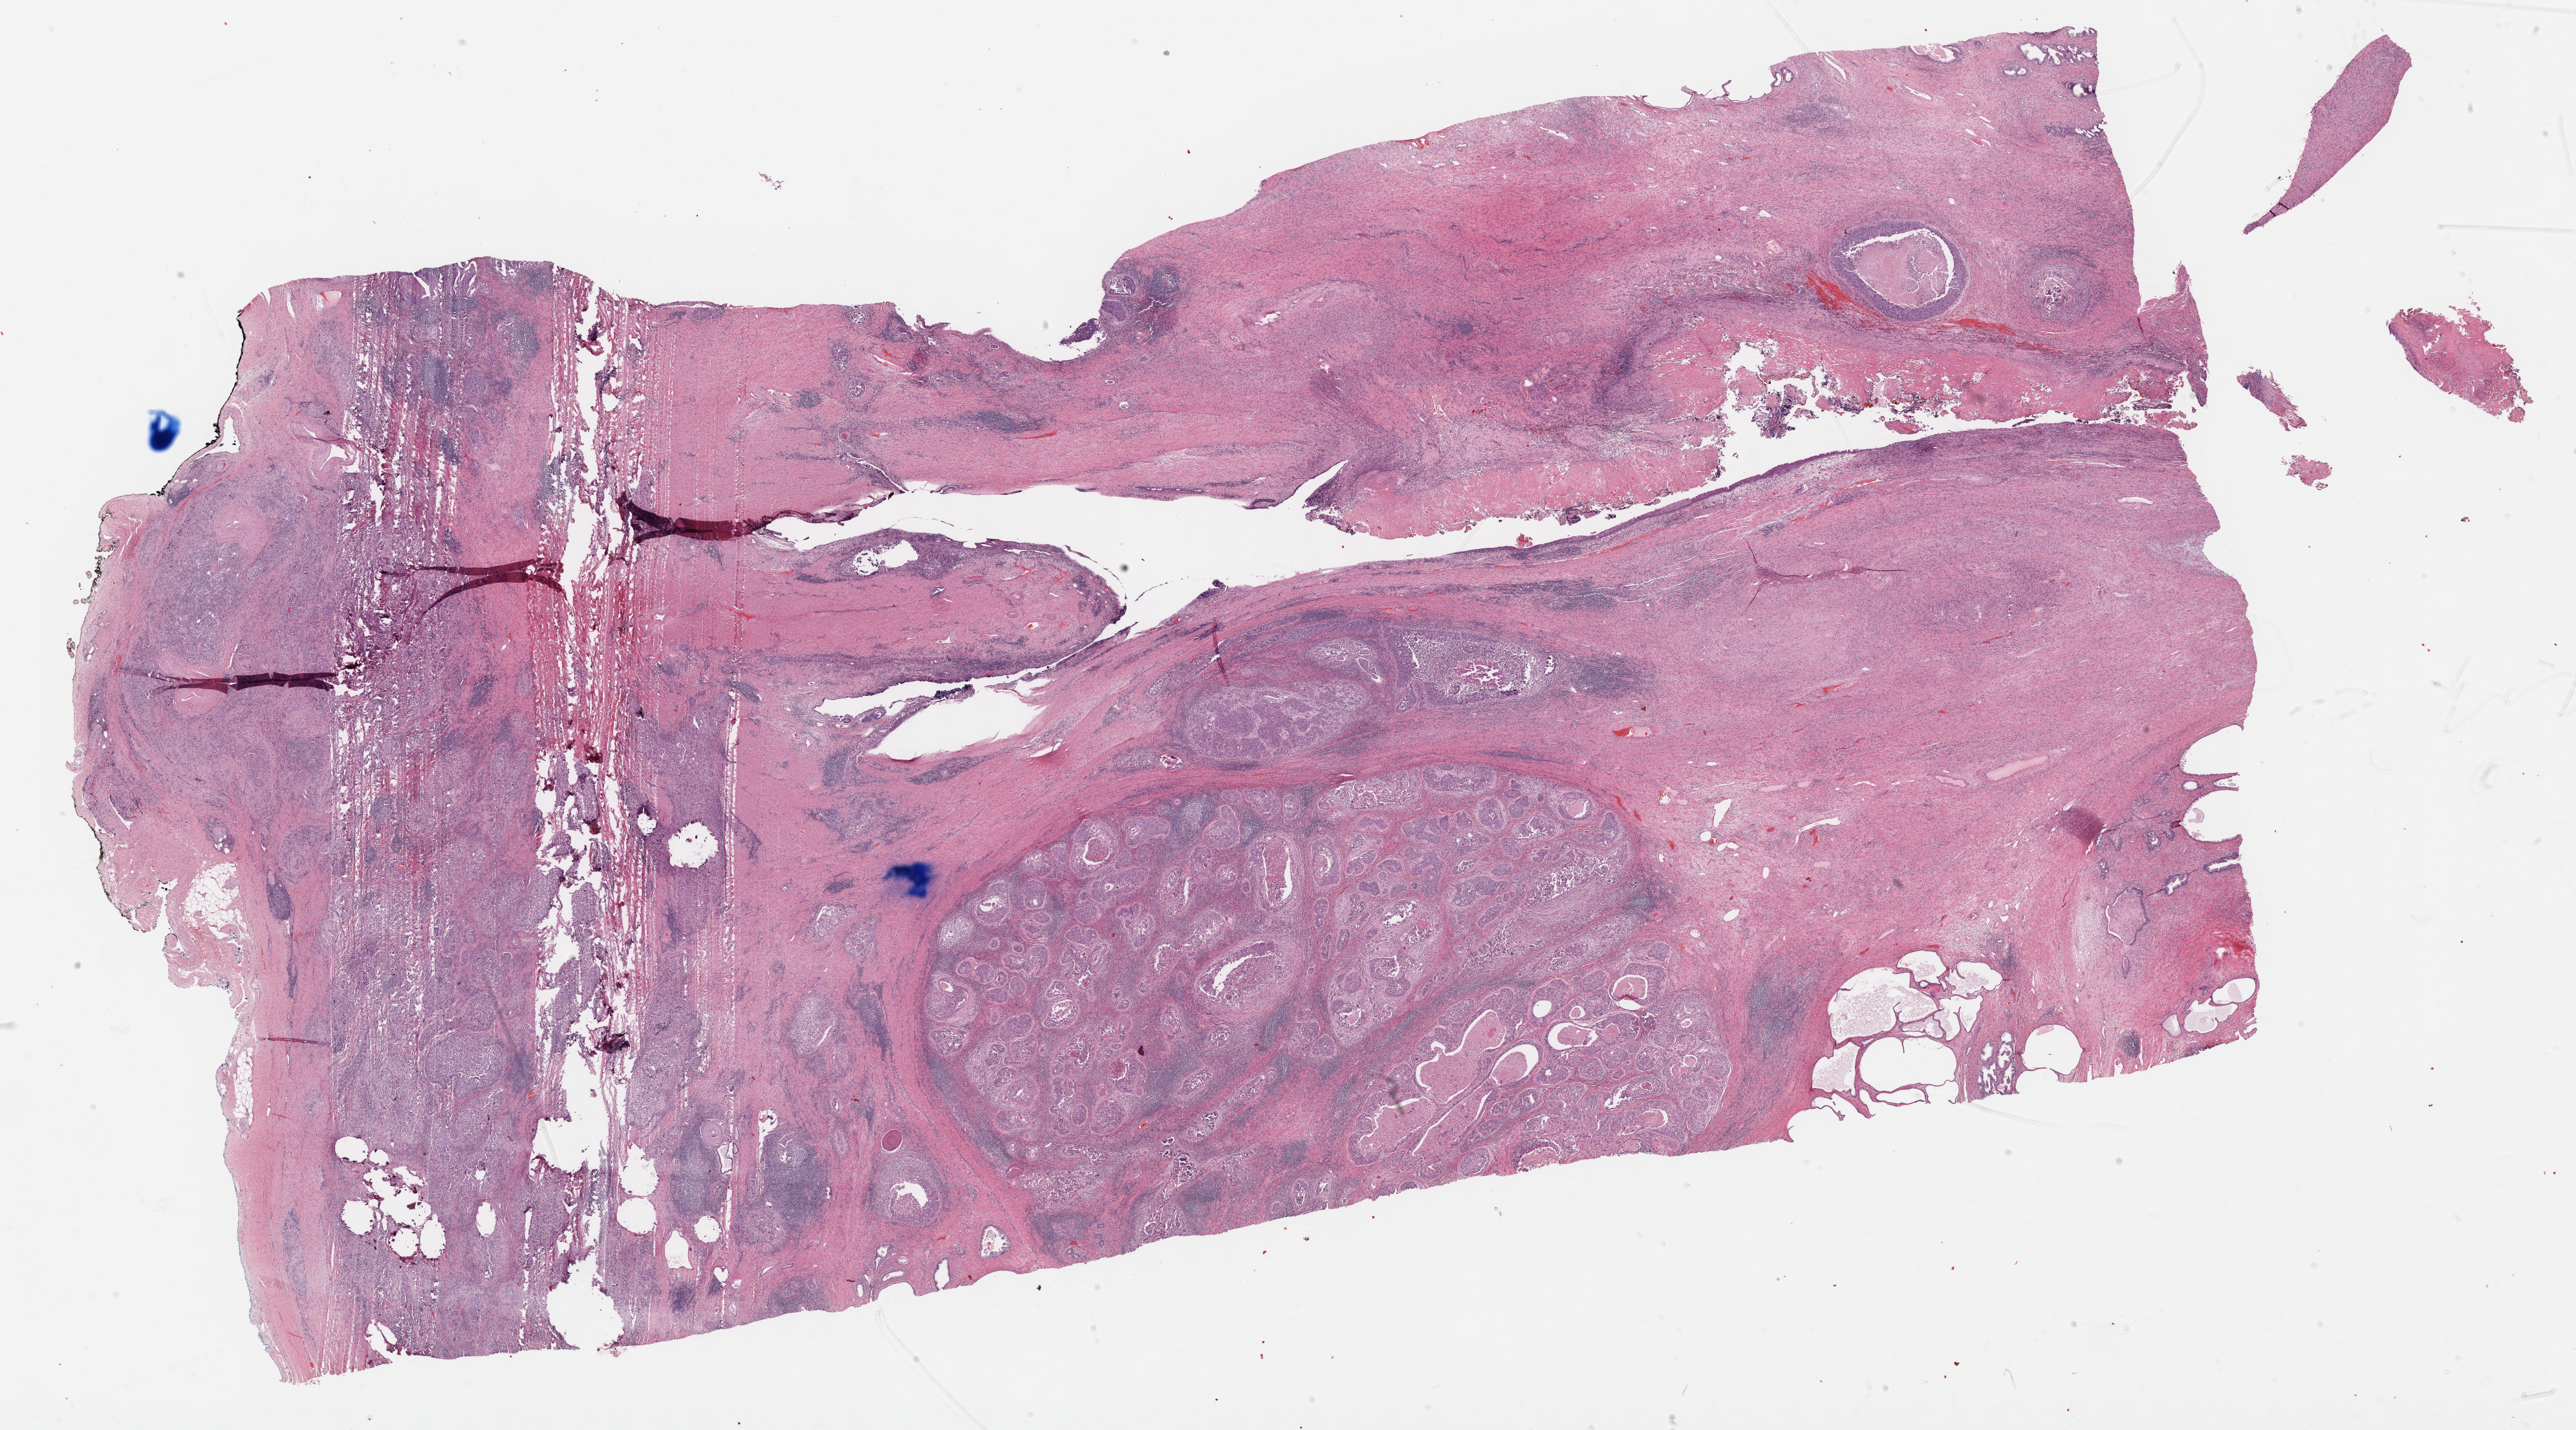
Whole-slide histology image, H&E, shown as a low-resolution overview of the whole scanned area (about 32.2 x 17.9 mm, from a 40x scan). Formalin-fixed paraffin-embedded (FFPE) diagnostic section. Primary tumour sample from the bladder. Patient: male, age at initial diagnosis 77 years.
• AJCC pathologic stage: IV
• diagnosis: Transitional cell carcinoma